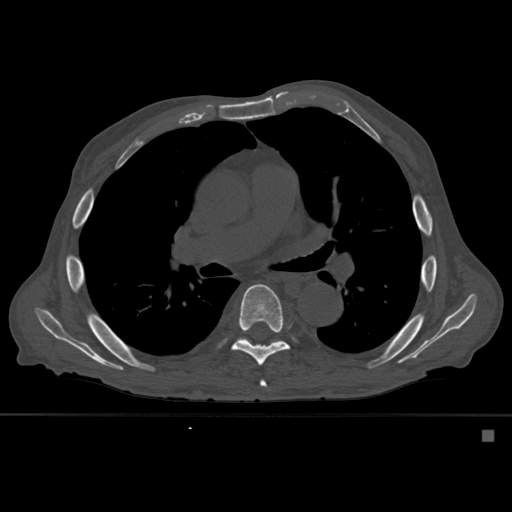
CT including the spine, one axial slice; slice 368 of 527 in the series (ordered by position); bone window (W 1800 / L 400 HU); 512 × 512 image matrix. Male patient, age 78 years. From the clinical record (not read from this slice): primary cancer: prostate.
Structures marked on this image (semi-automatic segmentation, software-assisted and operator-edited):
- T6 vertebra: bounding box [x1, y1, x2, y2] px = [260, 380, 267, 387]
- T7 vertebra: [216, 283, 290, 366]